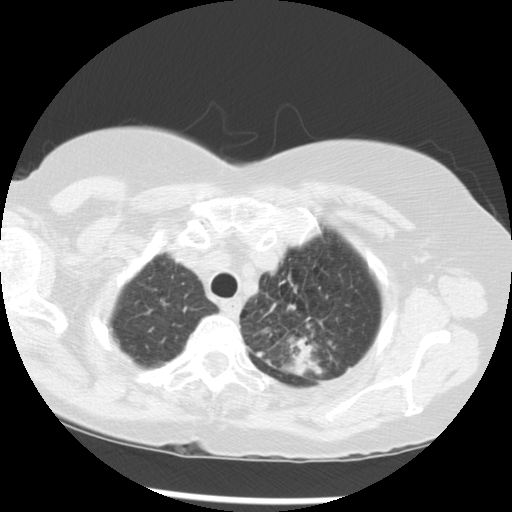
Low-dose screening chest CT, axial slice, third screening round (two years after baseline), lung window (W 1500 / L -600 HU), 2.5 mm slice thickness, standard (soft-tissue) reconstruction kernel (STANDARD), 120 kVp, slice 242 of 283 in the series. Female, age 70 years at enrolment.
• Expert-annotated lung lesion, box from (x=247, y=291) to (x=346, y=379) px.
• Reader record for this screening exam (exam-level; its link to the box is not recorded): non-calcified nodule or mass ≥4 mm, left upper lobe, 32 × 26 mm, spiculated (stellate) margins, soft tissue attenuation, pre-existing on the prior screen: yes; interval growth: yes.
• Official screen result: positive, other.